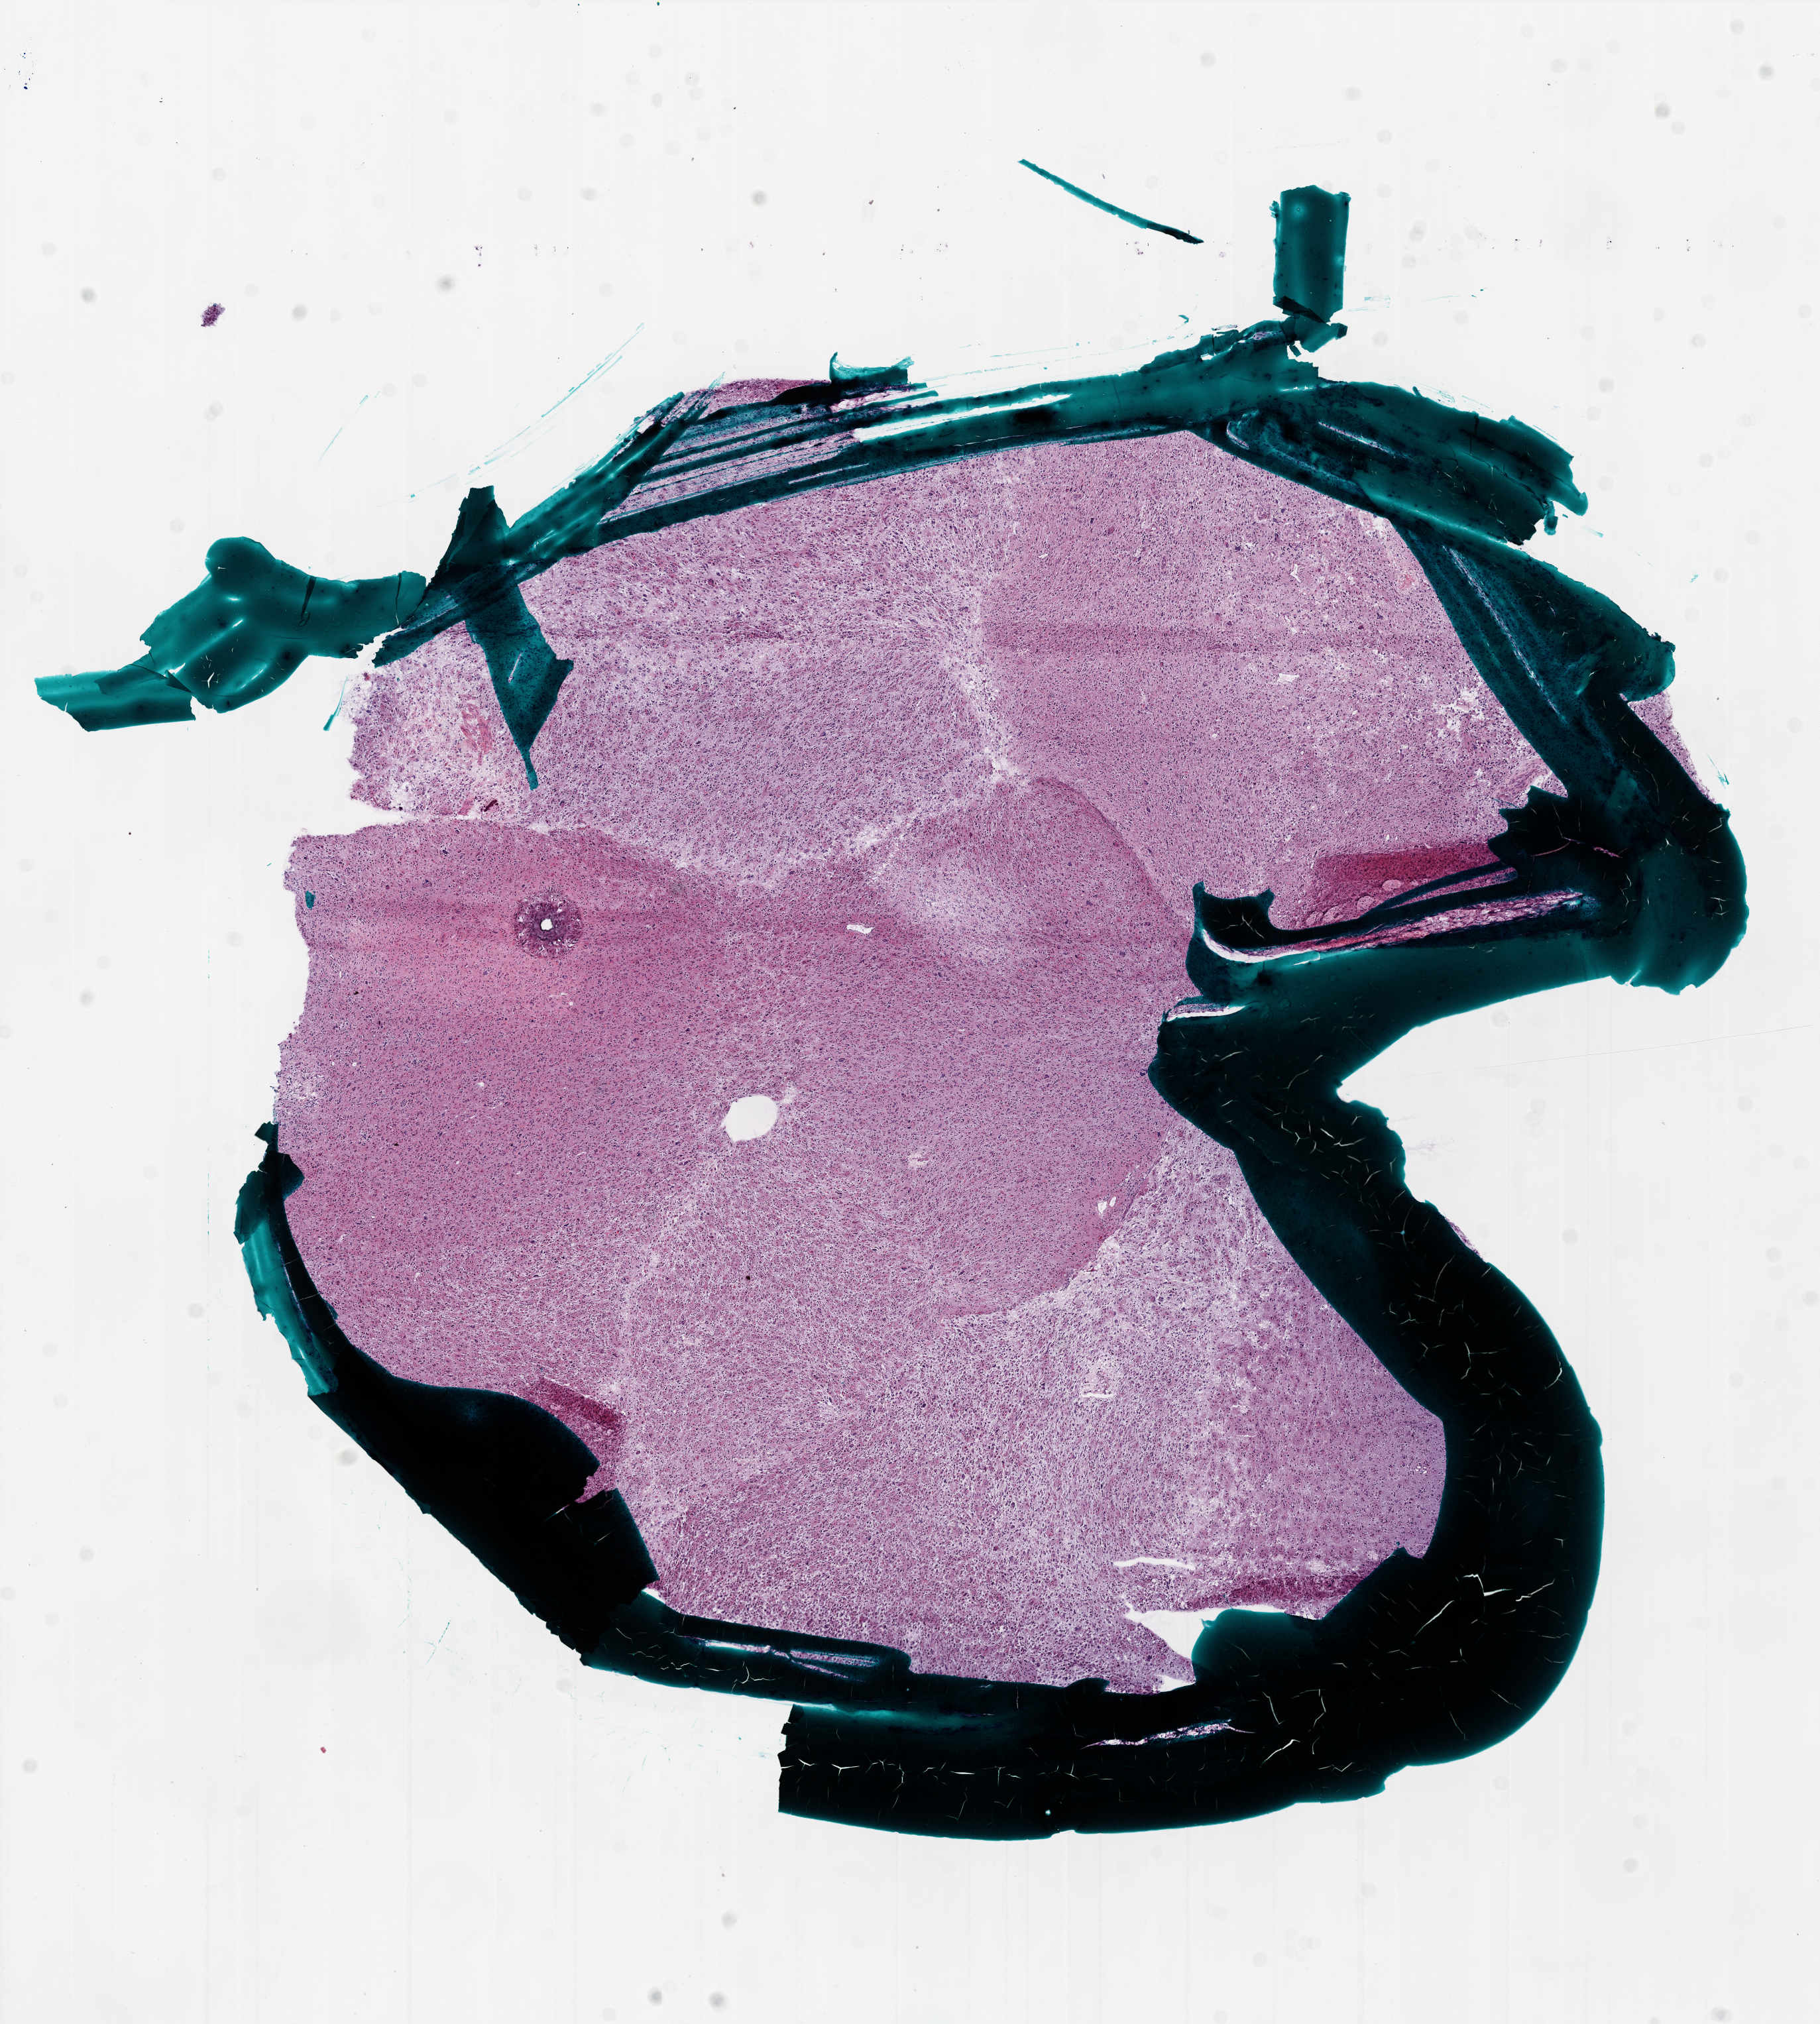
Digitized Hematoxylin and eosin (H&E) stained tissue section (whole slide) — a low-resolution overview of the entire scanned area, about 11.0 x 12.2 mm (slide scanned at 20x); frozen section; brain, primary tumour sample. Patient: female, age at initial diagnosis 75 years. Pathologist review of this section (percent, as recorded): tumour cells 95%, tumour nuclei 100%, normal cells 0%, stromal cells 0%, necrosis 5%.
Histologic diagnosis: Glioblastoma.